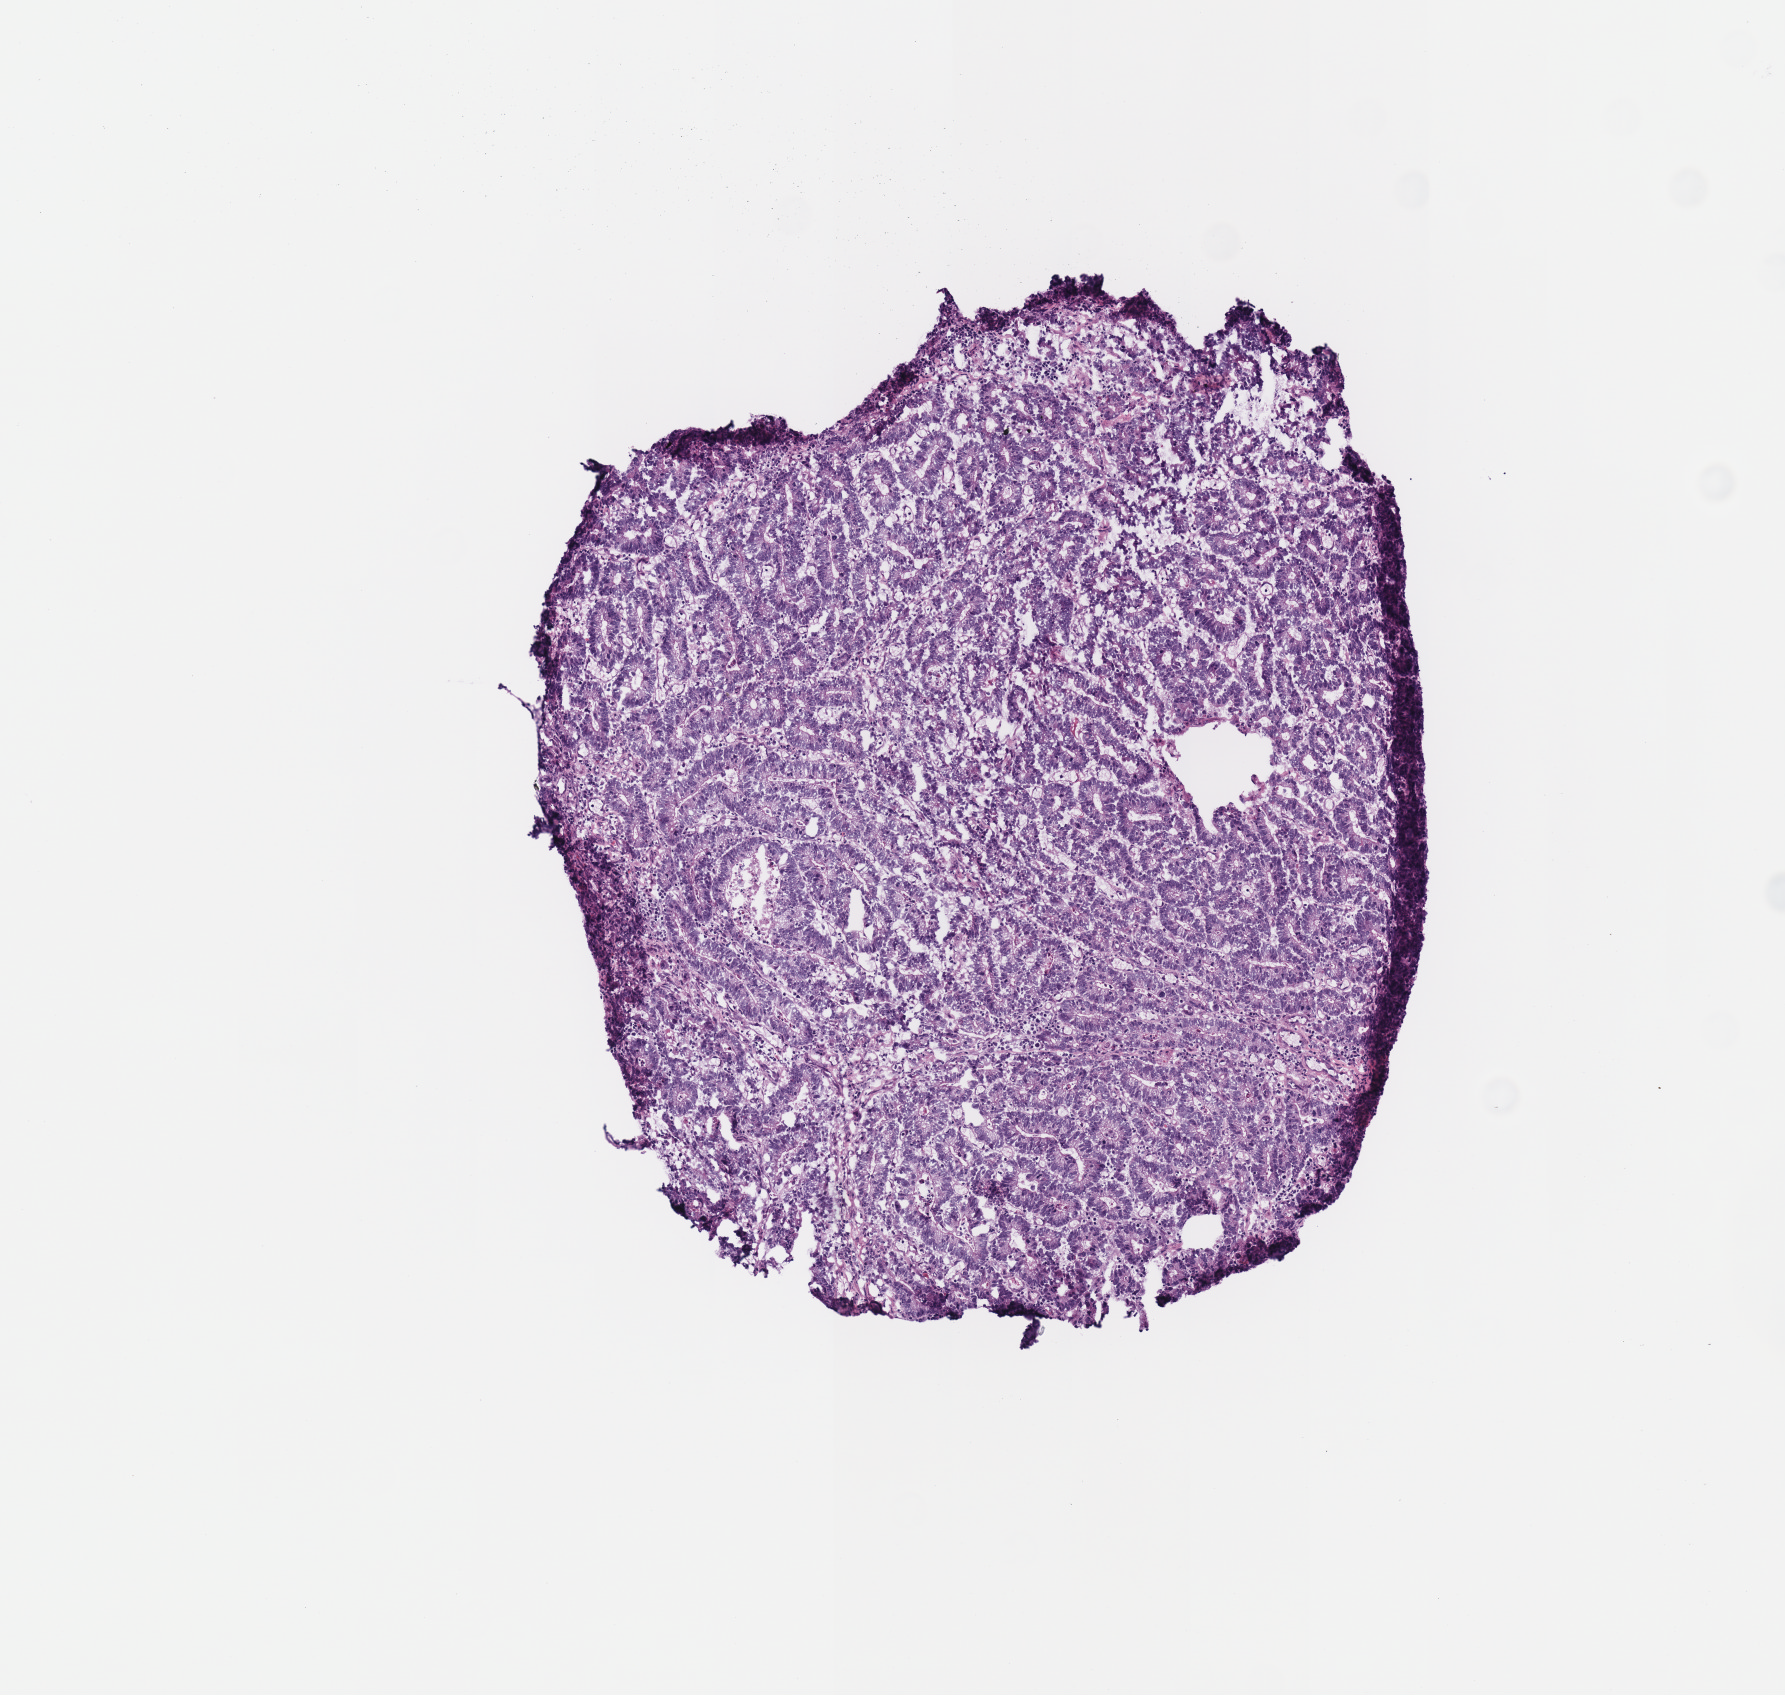
H&E-stained whole-slide image — a low-resolution overview of the entire scanned area, about 3.5 x 3.3 mm (from a 40x scan), frozen section from the top of the tissue portion, stomach, primary tumour sample. Patient: male, age at initial diagnosis 76 years. Histologic grade: G2 (moderately differentiated). Composition of this section per pathologist review: tumour cells 90%, tumour nuclei 80%, normal cells 0%, stromal cells 10%, necrosis 0%.
AJCC pathologic stage: IIIA. Diagnosis: Tubular adenocarcinoma. TNM: T3 N2 M0. Lymph nodes positive (case pathology): 5 of 99 examined.